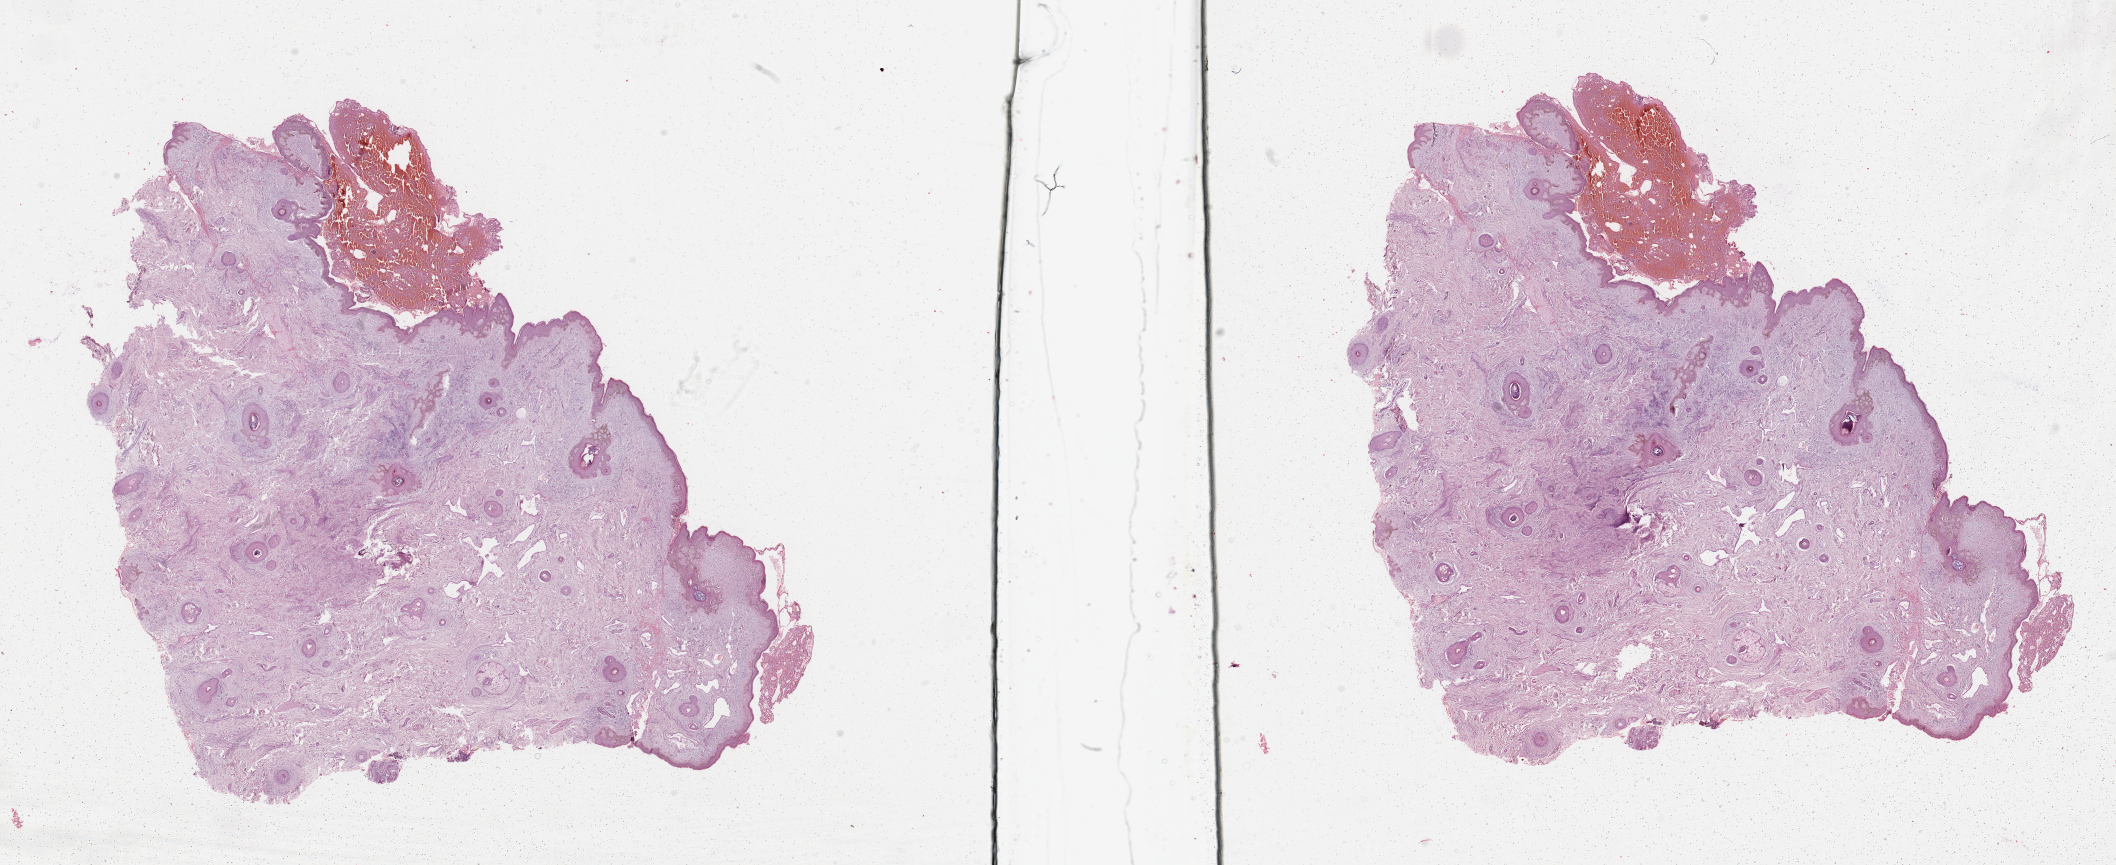
Whole-slide histology image, H&E, a low-resolution overview of the entire scanned area, about 33.5 x 13.7 mm (acquisition: 20x scan), normal (non-tumour) tissue sample, sampled site: shoulder. Male, 74 y/o.
This section: normal (non-tumour) tissue from the same patient. Patient diagnosis: Malignant melanoma, NOS.